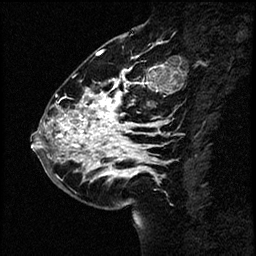
Breast MRI (dynamic contrast-enhanced), one sagittal slice. Slice 25 of 60 in the series (ordered by position). Dynamic contrast-enhanced study with each time point stored as its own series, time point 2 of 4 at this slice position (early post-contrast, ordered by acquisition time). 1.5 T. TE 4.2 ms, TR 17.6 ms. 2 mm slice thickness. 256 × 256 image matrix, field of view 200 × 200 mm. Patient: female, 43 years. Case-level facts recorded for this patient, not image findings: setting: breast cancer imaged before/during neoadjuvant chemotherapy.
Structures marked on this image (semi-automatic segmentation, software-assisted and operator-edited):
- analysis volume of interest (the breast-tissue region the enhancement analysis was run in; not a lesion): bounding box (x1, y1, x2, y2) in pixels: (34, 56, 169, 191)
- tumour enhancement mask (voxels above the 100 % enhancement threshold inside the analysis volume of interest): (35, 69, 164, 178)